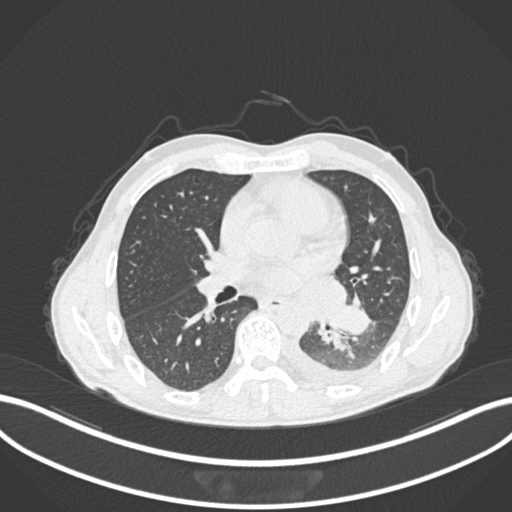
Chest CT, one axial slice. Position 122 of 222 along the scan axis. Lung window (W 1500 / L -600 HU). 512 × 512 image matrix, field of view 400 × 400 mm. Patient: male, 47 years. Case-level facts recorded for this patient, not image findings: clinical TNM (as recorded): T3 N1 M1c; histopathological grade: G3.
Annotated regions visible in this slice (rectangle marked by the reading radiologist):
- lung tumour (recorded histology: small cell carcinoma): bounding box [x1, y1, x2, y2] px = [326, 299, 374, 338]